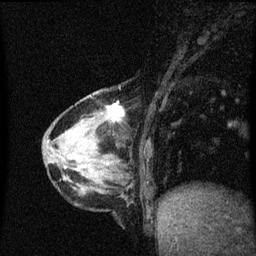
Breast MRI (dynamic contrast-enhanced), one sagittal slice; dynamic contrast-enhanced series, image 2 of 3 at this slice position (ordered by acquisition); 1.5 T; TE 4.2 ms, TR 8.4 ms; 256 × 256 image matrix, field of view 200 × 200 mm. Patient: female, 64 years. From the clinical record (not read from this slice): setting: breast cancer imaged before/during neoadjuvant chemotherapy; receptor status: HR-positive, HER2-negative.
Annotated regions visible in this slice (semi-automatic segmentation, software-assisted and operator-edited):
- analysis volume of interest (the breast-tissue region the enhancement analysis was run in; not a lesion): bounding box (x1, y1, x2, y2) in pixels: (65, 96, 126, 157)
- tumour enhancement mask (voxels above the 70 % enhancement threshold inside the analysis volume of interest): (107, 104, 125, 121)